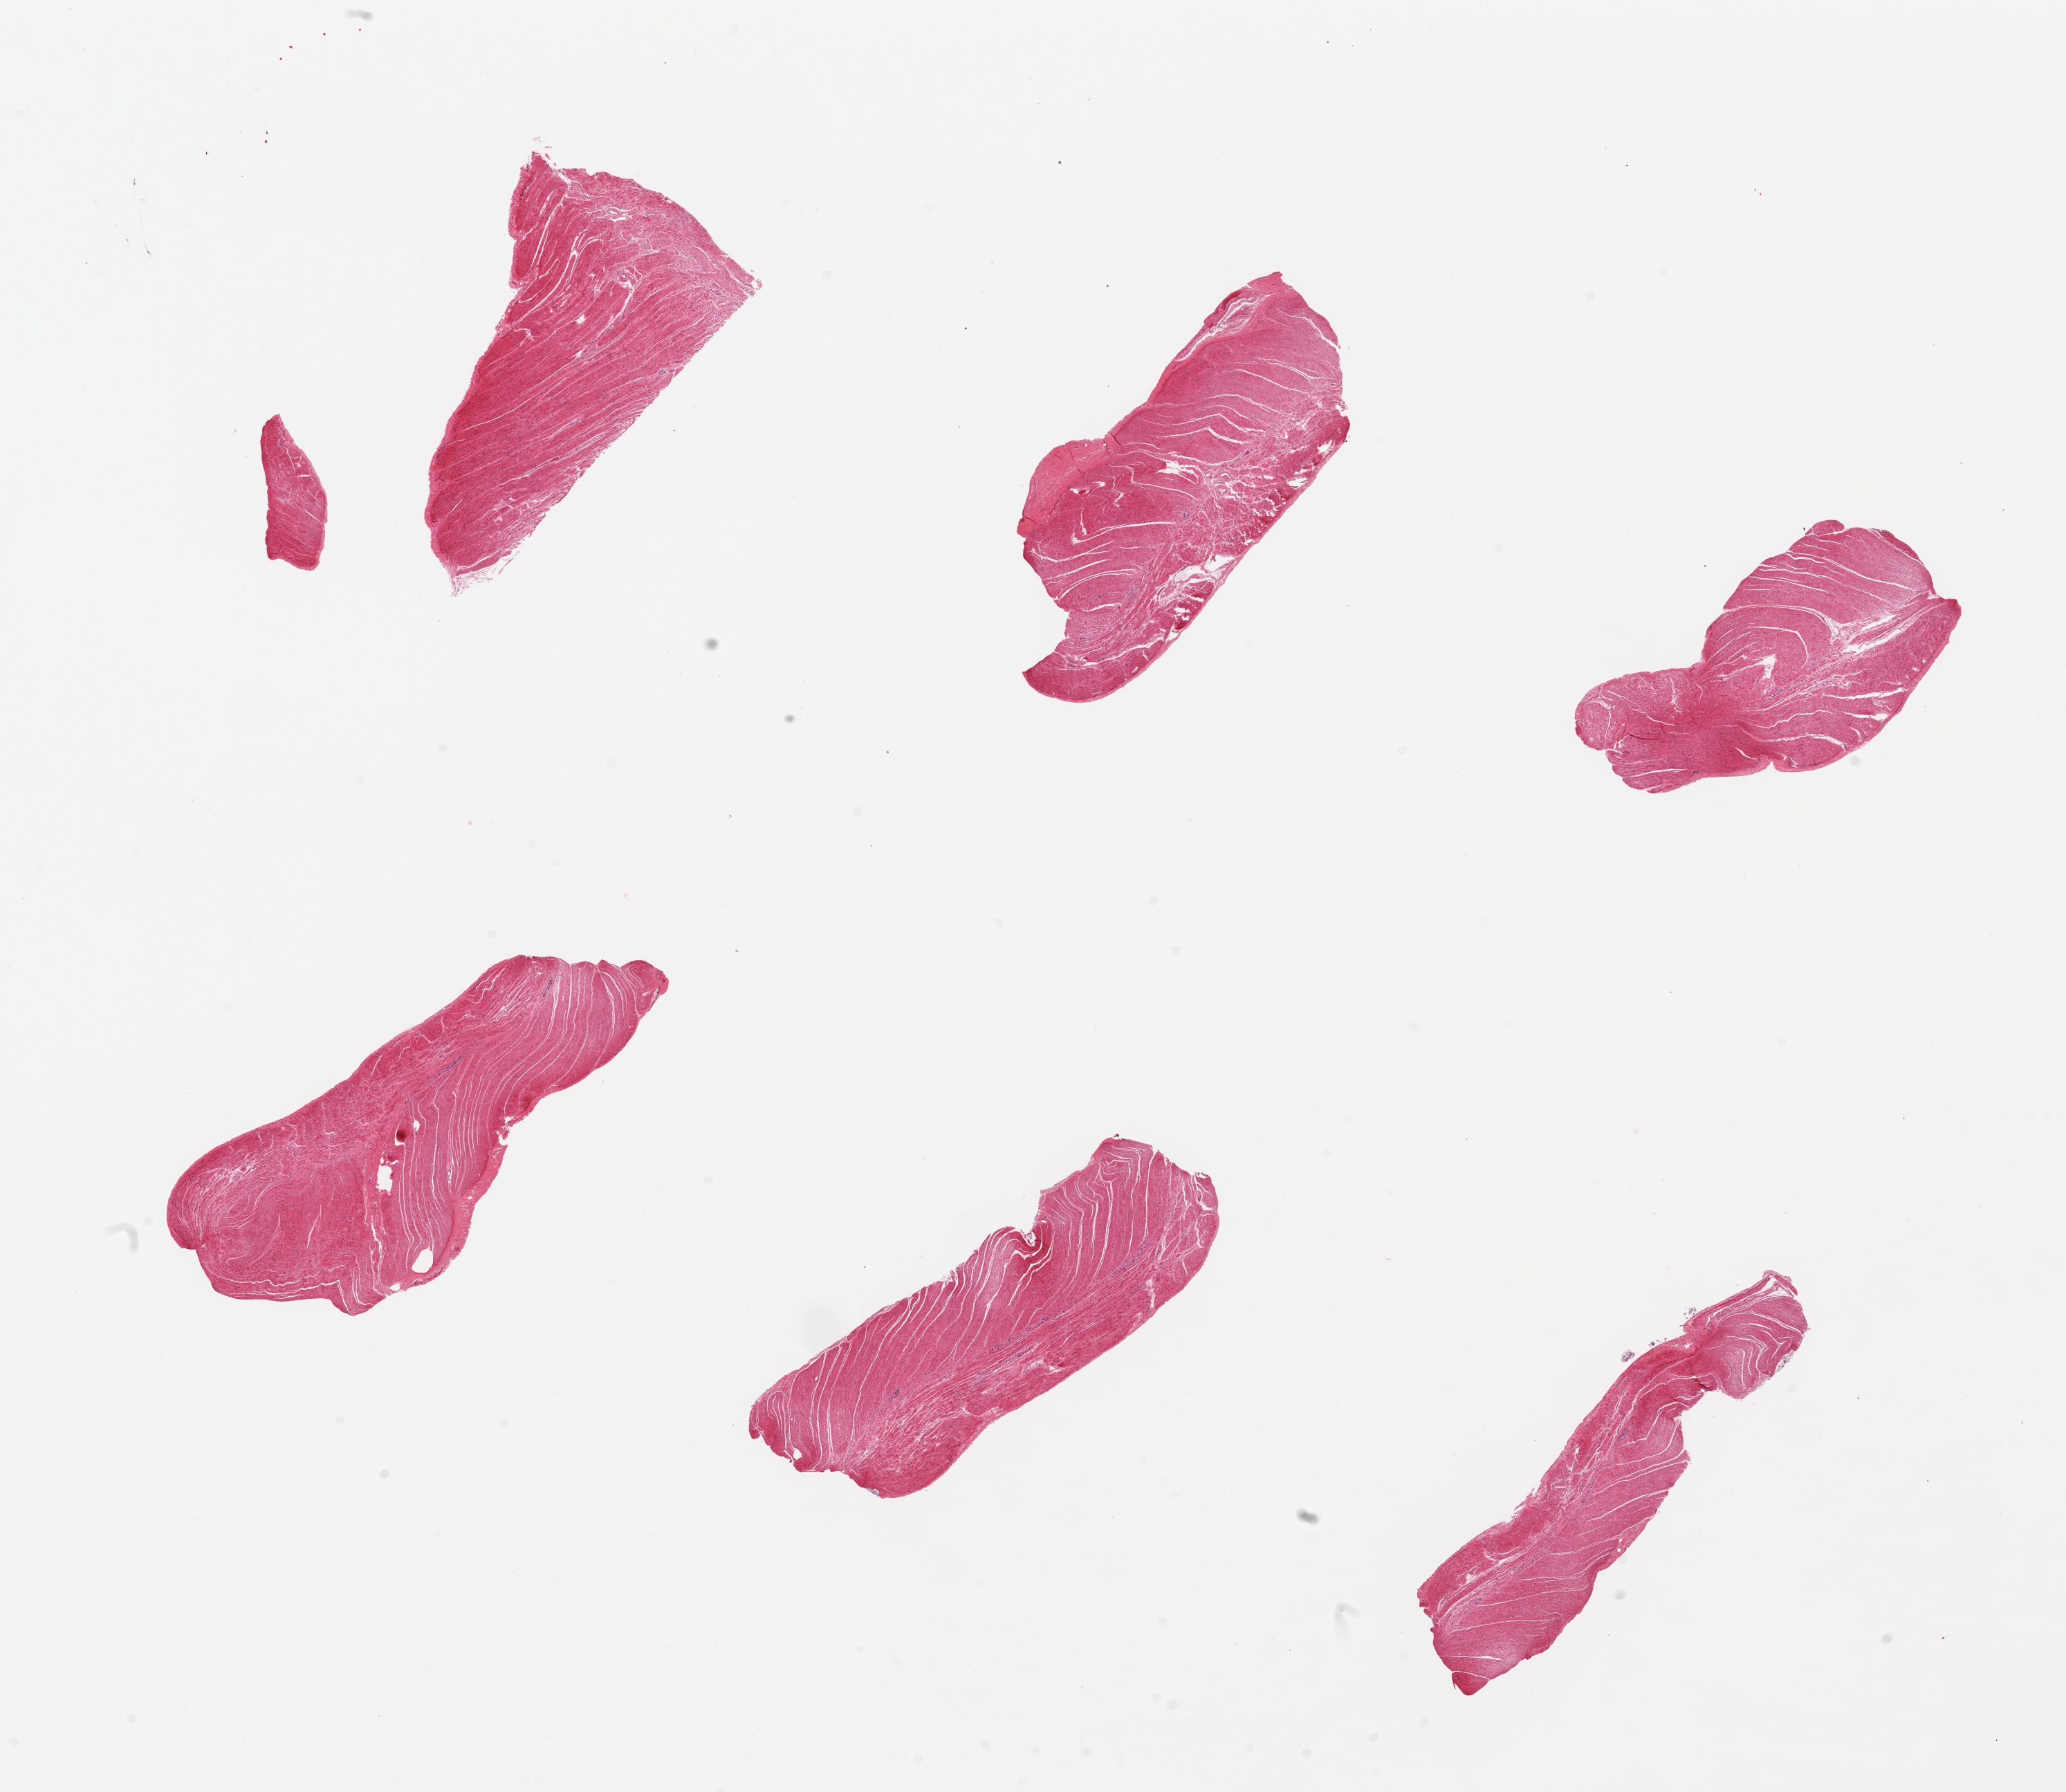
Haematoxylin and eosin whole-slide image — shown as a low-resolution overview of the whole scanned area (about 23.6 x 20.5 mm, from a 20x scan), PAXgene-fixed, paraffin-embedded tissue, target tissue: sigmoid colon, donor tissue sample.
- pathologist's review note for this sample: 6 pieces, all muscularis